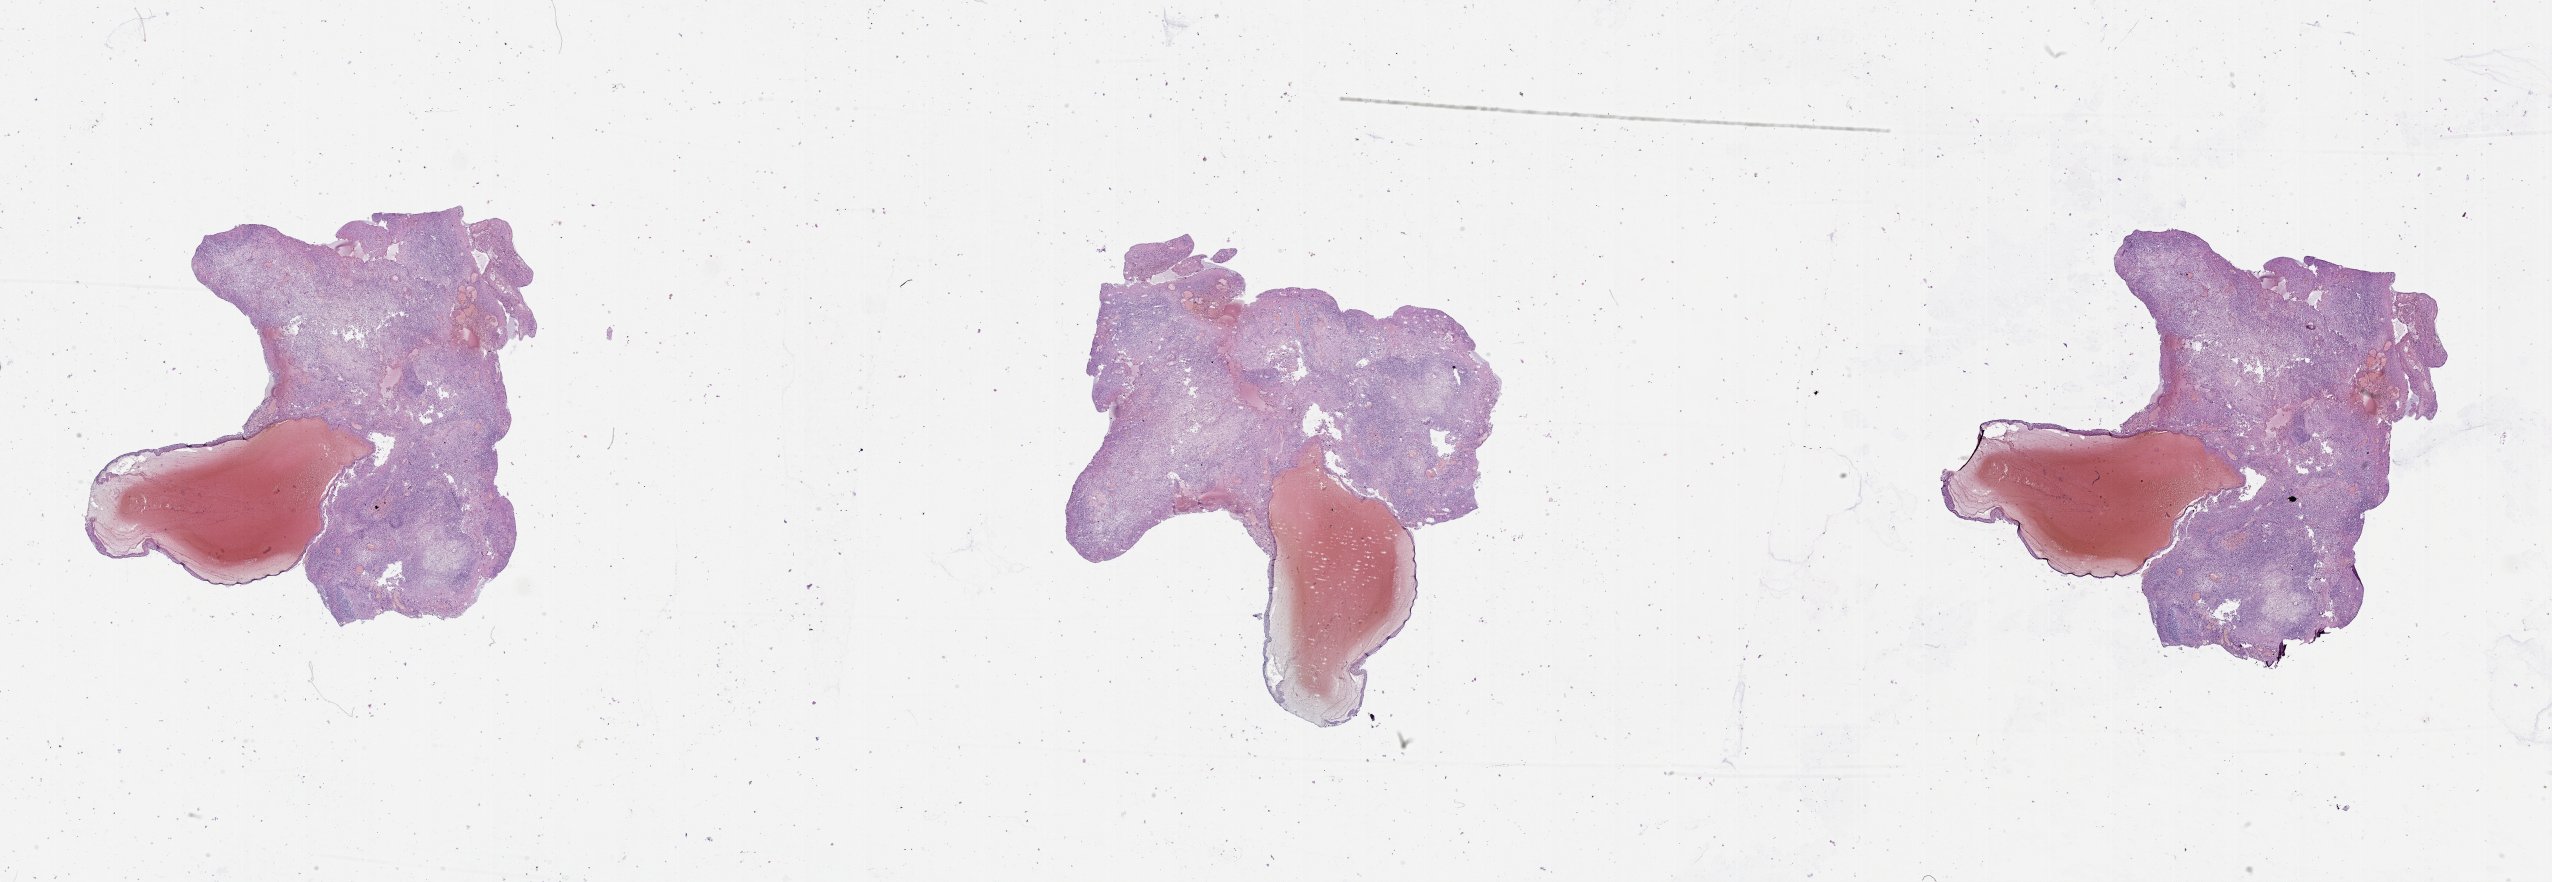
Whole-slide histology image, H&E-stained — whole scanned area (about 41.1 x 14.2 mm) shown as a low-resolution overview; brain, tumour tissue. Male, 63 y/o.
Primary tumour site (as recorded): frontal lobe. Diagnosis: Glioblastoma.